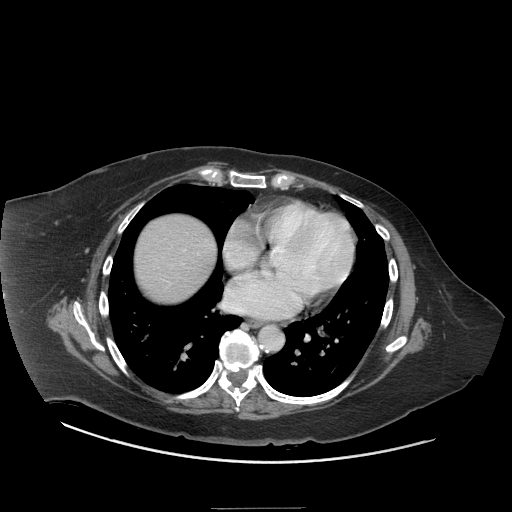
Contrast-enhanced abdominal CT (liver protocol), one axial slice. Slice 73 of 81 in the series (ordered by position). 140 kVp. Soft-tissue window (W 400 / L 40 HU). 2.5 mm slice thickness. 512 × 512 image matrix, field of view 440 × 440 mm. From the clinical record (not read from this slice): diagnosis: hepatocellular carcinoma (patient treated with transarterial chemoembolisation; whether this scan precedes or follows treatment is not stated here); TNM stage (as recorded): Stage-II.
Outlined on this slice (semi-automatically segmented with operator editing):
- liver parenchyma outside the tumour (the mass and vessels are separate outlines, so this box may not span the whole liver): box from (x=135, y=214) to (x=216, y=300) px
- liver vessels: (x=169, y=249)–(x=199, y=284)